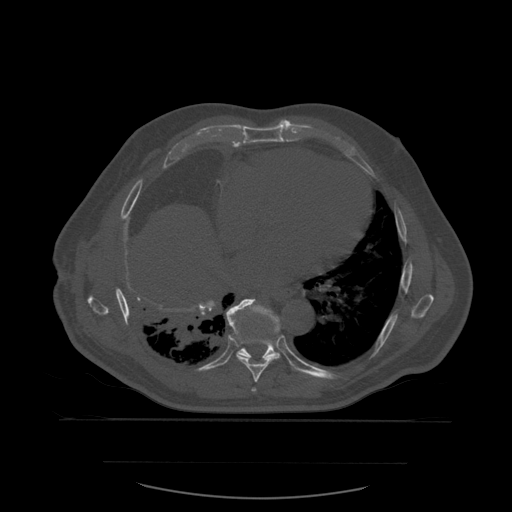
CT including the spine, one axial slice. Position 353 of 590 along the scan axis. Bone window (W 1800 / L 400 HU). 1.25 mm slice thickness. 512 × 512 image matrix. Patient age 71 years. Case-level facts recorded for this patient, not image findings: primary cancer: lung; vertebrae with lytic lesions (as recorded): T1, T2, L5, S1.
Annotated regions visible in this slice (semi-automatically segmented with operator editing):
- T7 vertebra: bounding box <252,388,257,392> (left, top, right, bottom; pixels)
- T8 vertebra: <226,300,281,383>
- T9 vertebra: <231,299,281,361>